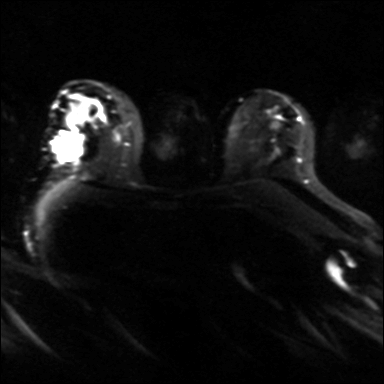
Breast MRI, one axial slice. Position 25 of 36 along the scan axis. Diffusion-weighted series; image 2 of 4 stored at this slice position (different b-values; order by instance number). 3 T. 4 mm slice thickness. 384 × 384 image matrix, field of view 320 × 320 mm. Female patient.
Annotated regions visible in this slice (manually delineated by an expert):
- tumour on diffusion-weighted imaging: bounding box (x1, y1, x2, y2) in pixels: (53, 135, 80, 160)